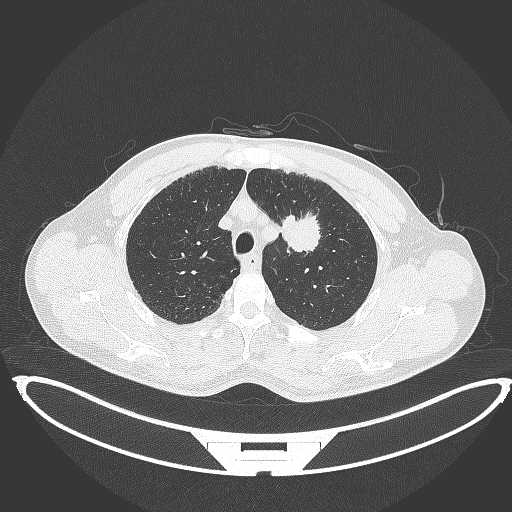
Chest CT, one axial slice. Reconstruction kernel B70f. Lung window (W 1500 / L -600 HU). 1 mm slice thickness. 512 × 512 image matrix, field of view 457 × 457 mm. Patient: male, 60 years. Case-level facts recorded for this patient, not image findings: clinical TNM (as recorded): T2a N0 M0; histopathological grade: G1-G2.
Outlined on this slice (bounding box drawn by a radiologist):
- lung tumour (recorded histology: squamous cell carcinoma): box from (x=280, y=212) to (x=321, y=255) px